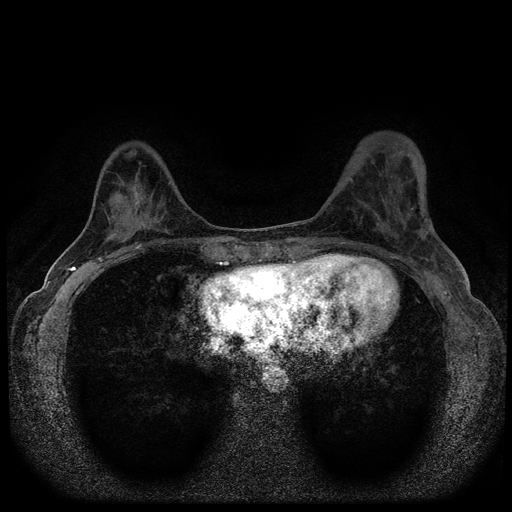
Breast MRI (dynamic contrast-enhanced, multi-phase), one axial slice. Slice 36 of 116 in the series (ordered by position). Dynamic contrast-enhanced series, time point 2 of 5 at this slice position (early post-contrast). 1.5 T. TE 2.7 ms, TR 5.6 ms. 512 × 512 image matrix. Patient: female, 40 years.
Outlined on this slice (semi-automatic segmentation, software-assisted and operator-edited):
- breast lesion (labelled benign in the annotation): bounding box (x1, y1, x2, y2) in pixels: (131, 189, 144, 207)